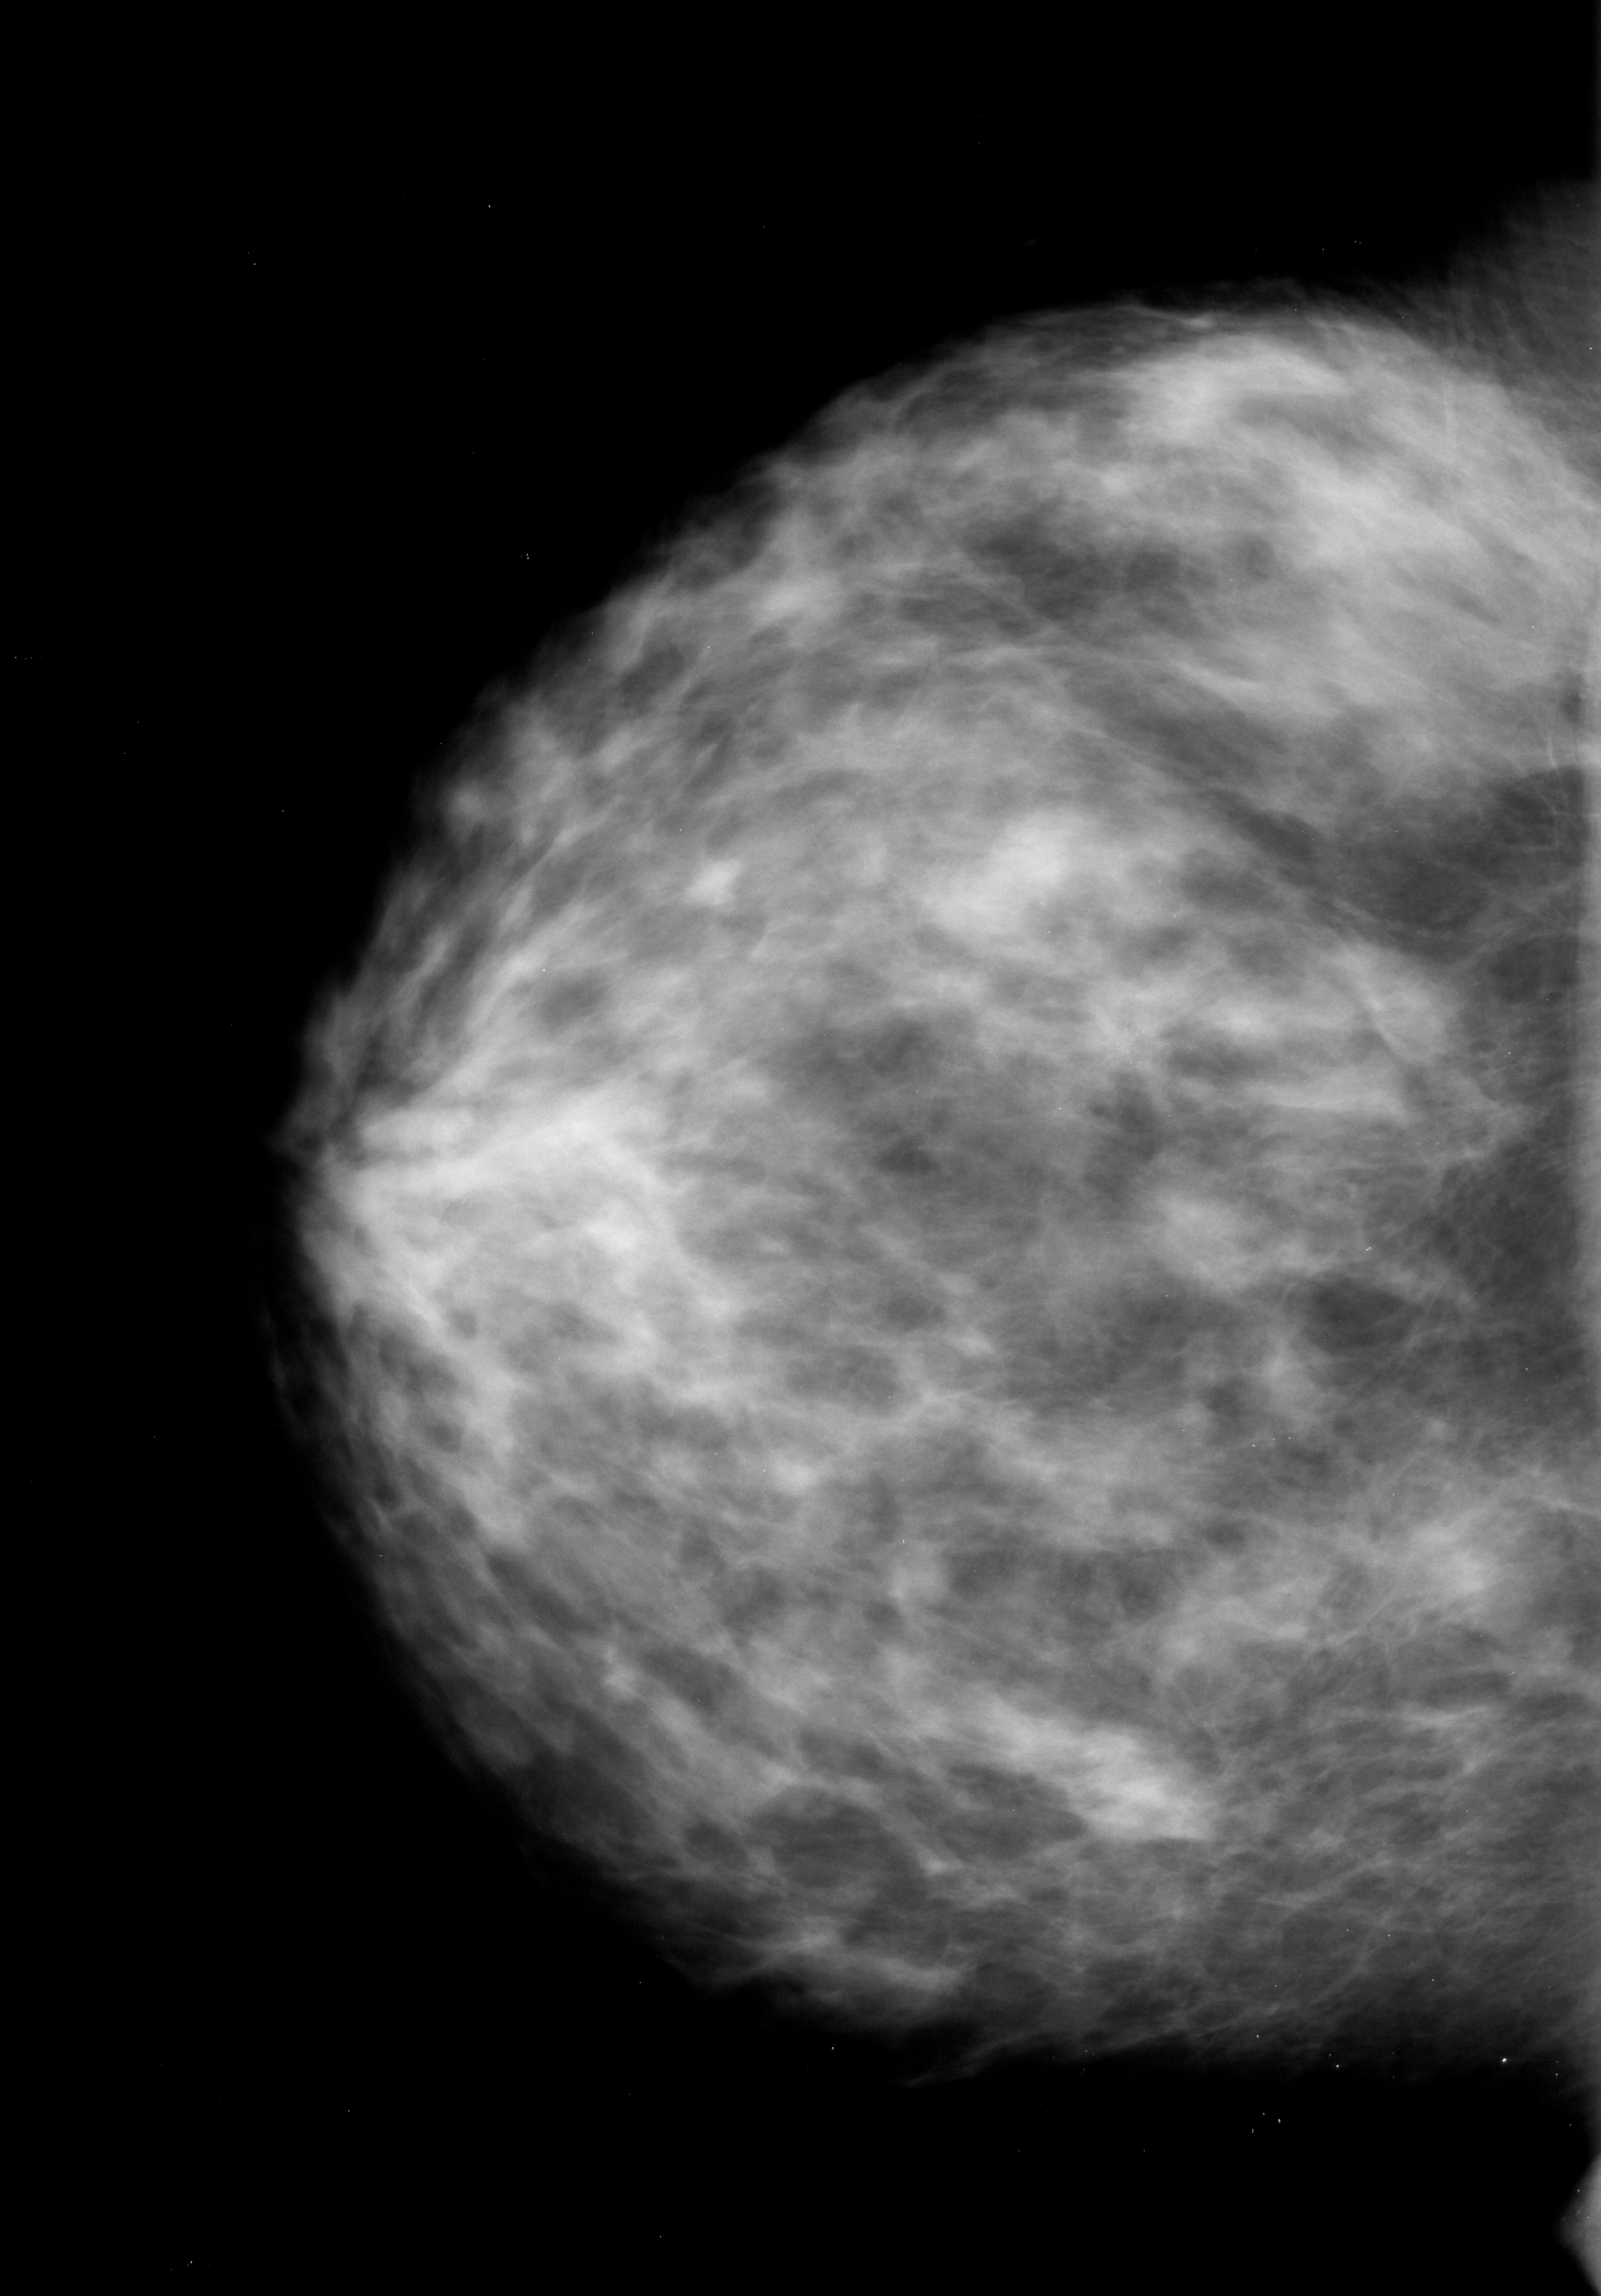
Digitized screen-film mammogram. Left breast. Craniocaudal (CC) view. Breast composition: extremely dense (BI-RADS density category 4 of 4). 1601 × 2296 image matrix.
Expert-marked regions of interest on this film, with their recorded descriptors:
- calcifications, morphology pleomorphic, distribution clustered; BI-RADS assessment category 4; subtlety rating 1 on a 1 (subtle) to 5 (obvious) scale; pathology (as recorded): malignant: bounding box (x1, y1, x2, y2) in pixels: (1086, 993, 1210, 1060)